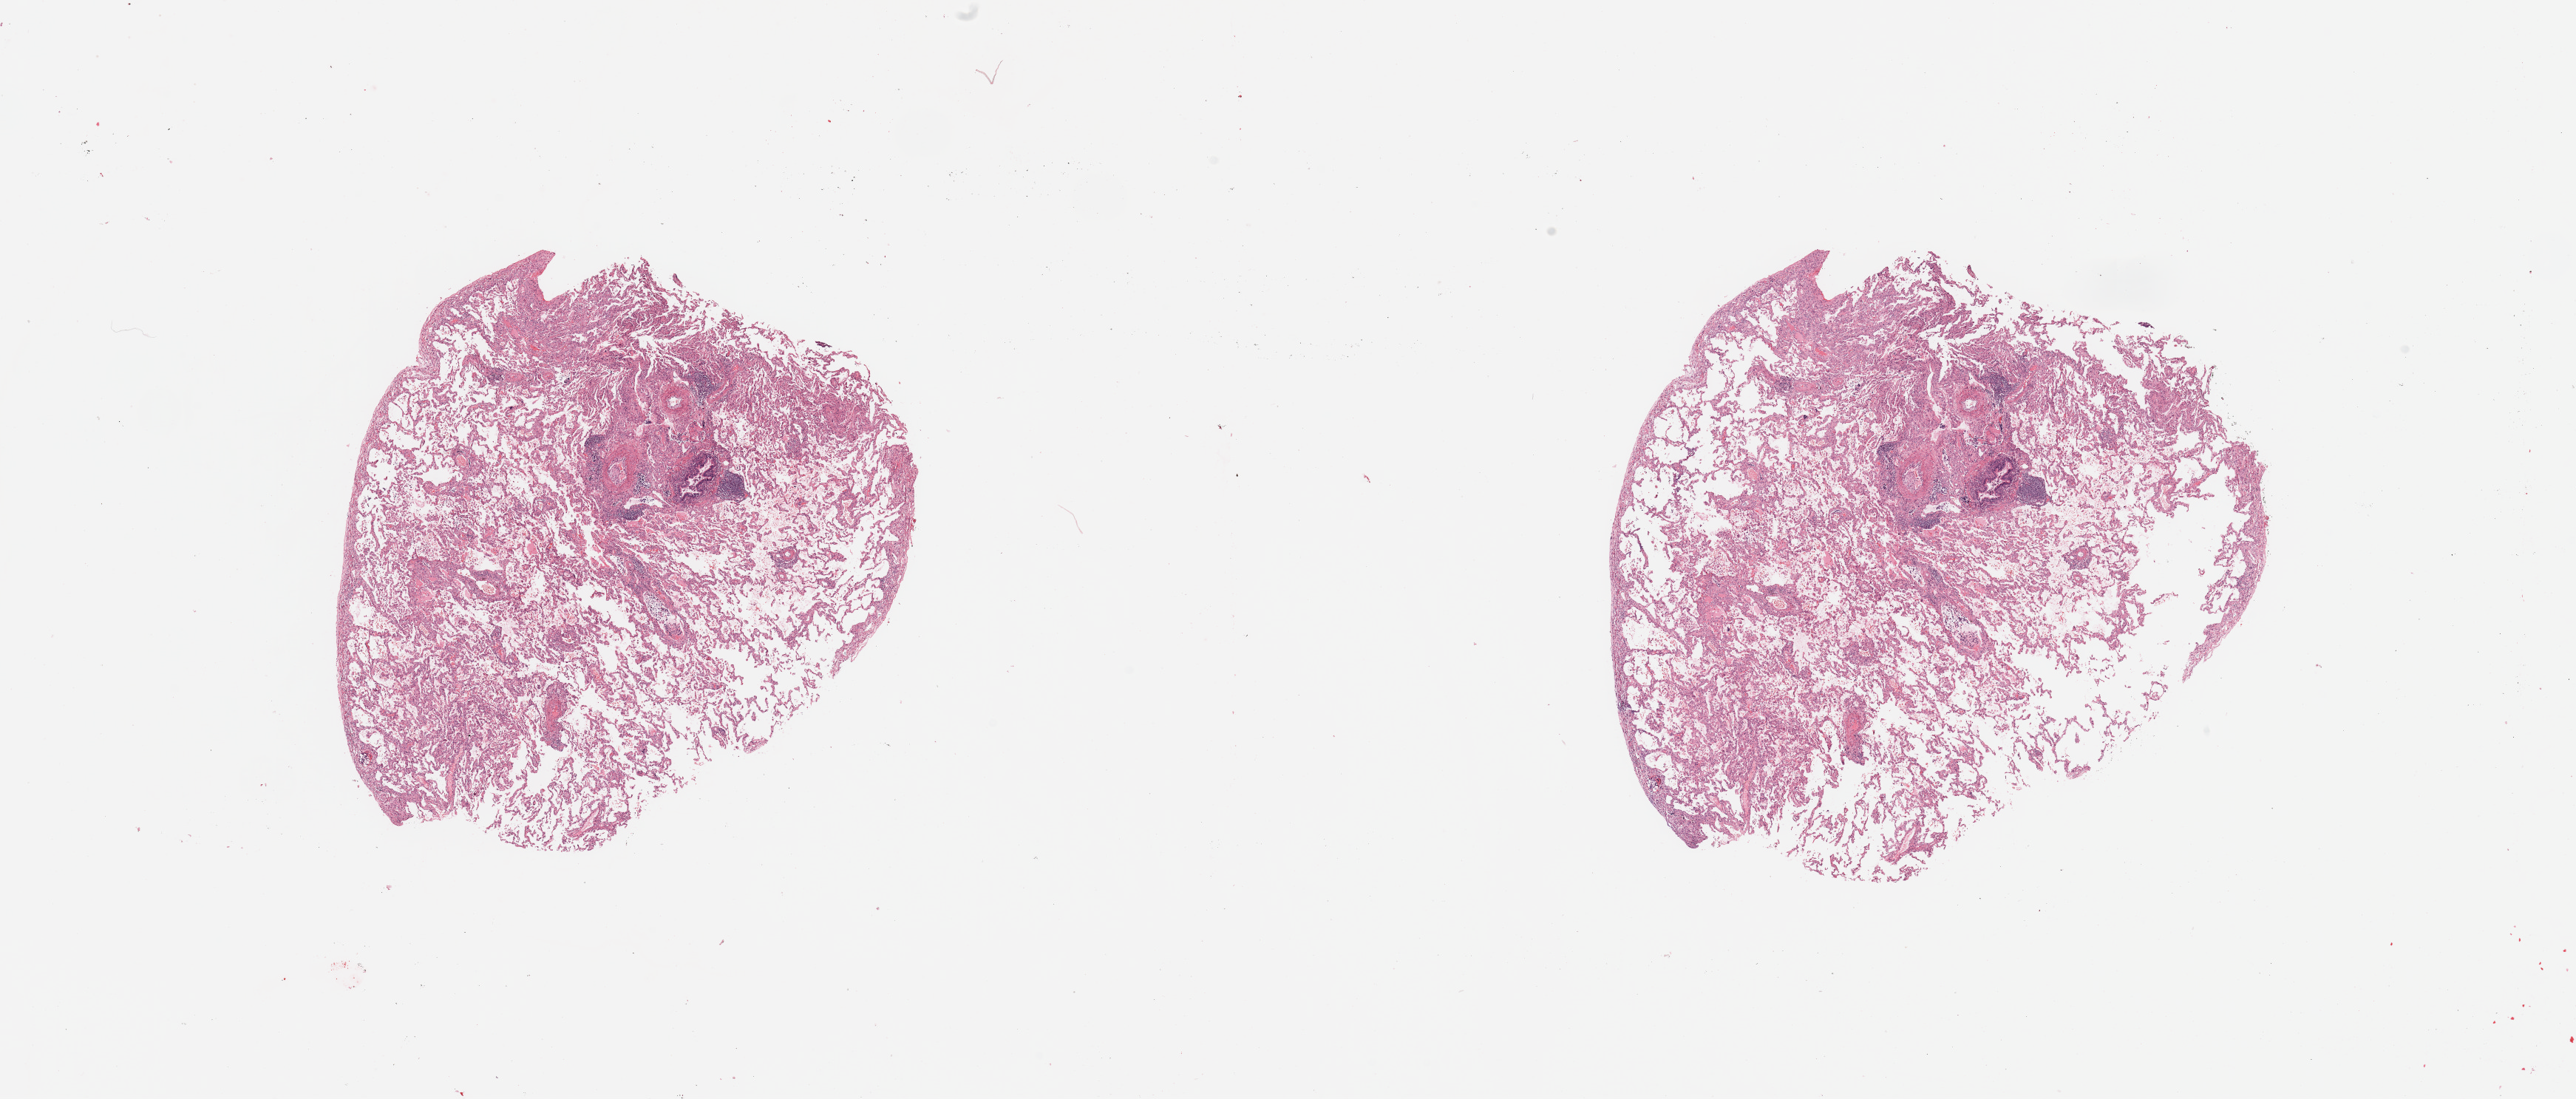
Digitized H&E tissue section (whole slide), low-resolution overview of the scanned area, about 27.6 x 11.8 mm (acquisition: 20x scan); lung, normal (non-tumour) tissue. Patient: male, age 63 years.
This section: normal (non-tumour) tissue from the same patient. Patient diagnosis: Adenocarcinoma, NOS.